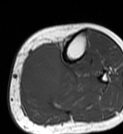
MRI of an extremity soft-tissue mass, one axial slice; slice 23 of 68 in the series (ordered by position); MR volume resampled by the dataset authors to the PET/CT grid (not the native acquisition matrix); 3.27 mm slice thickness; 123 × 134 image matrix, field of view 120 × 131 mm. Female patient. From the clinical record (not read from this slice): histological type: extraskeletal high grade osteogenic sarcoma; grade: high; site of the primary tumour: left calf.
Outlined on this slice (expert contour drawn on MRI and transferred to this co-registered scan by the dataset authors):
- gross tumour volume (mass): bounding box [x1, y1, x2, y2] px = [22, 45, 62, 101]